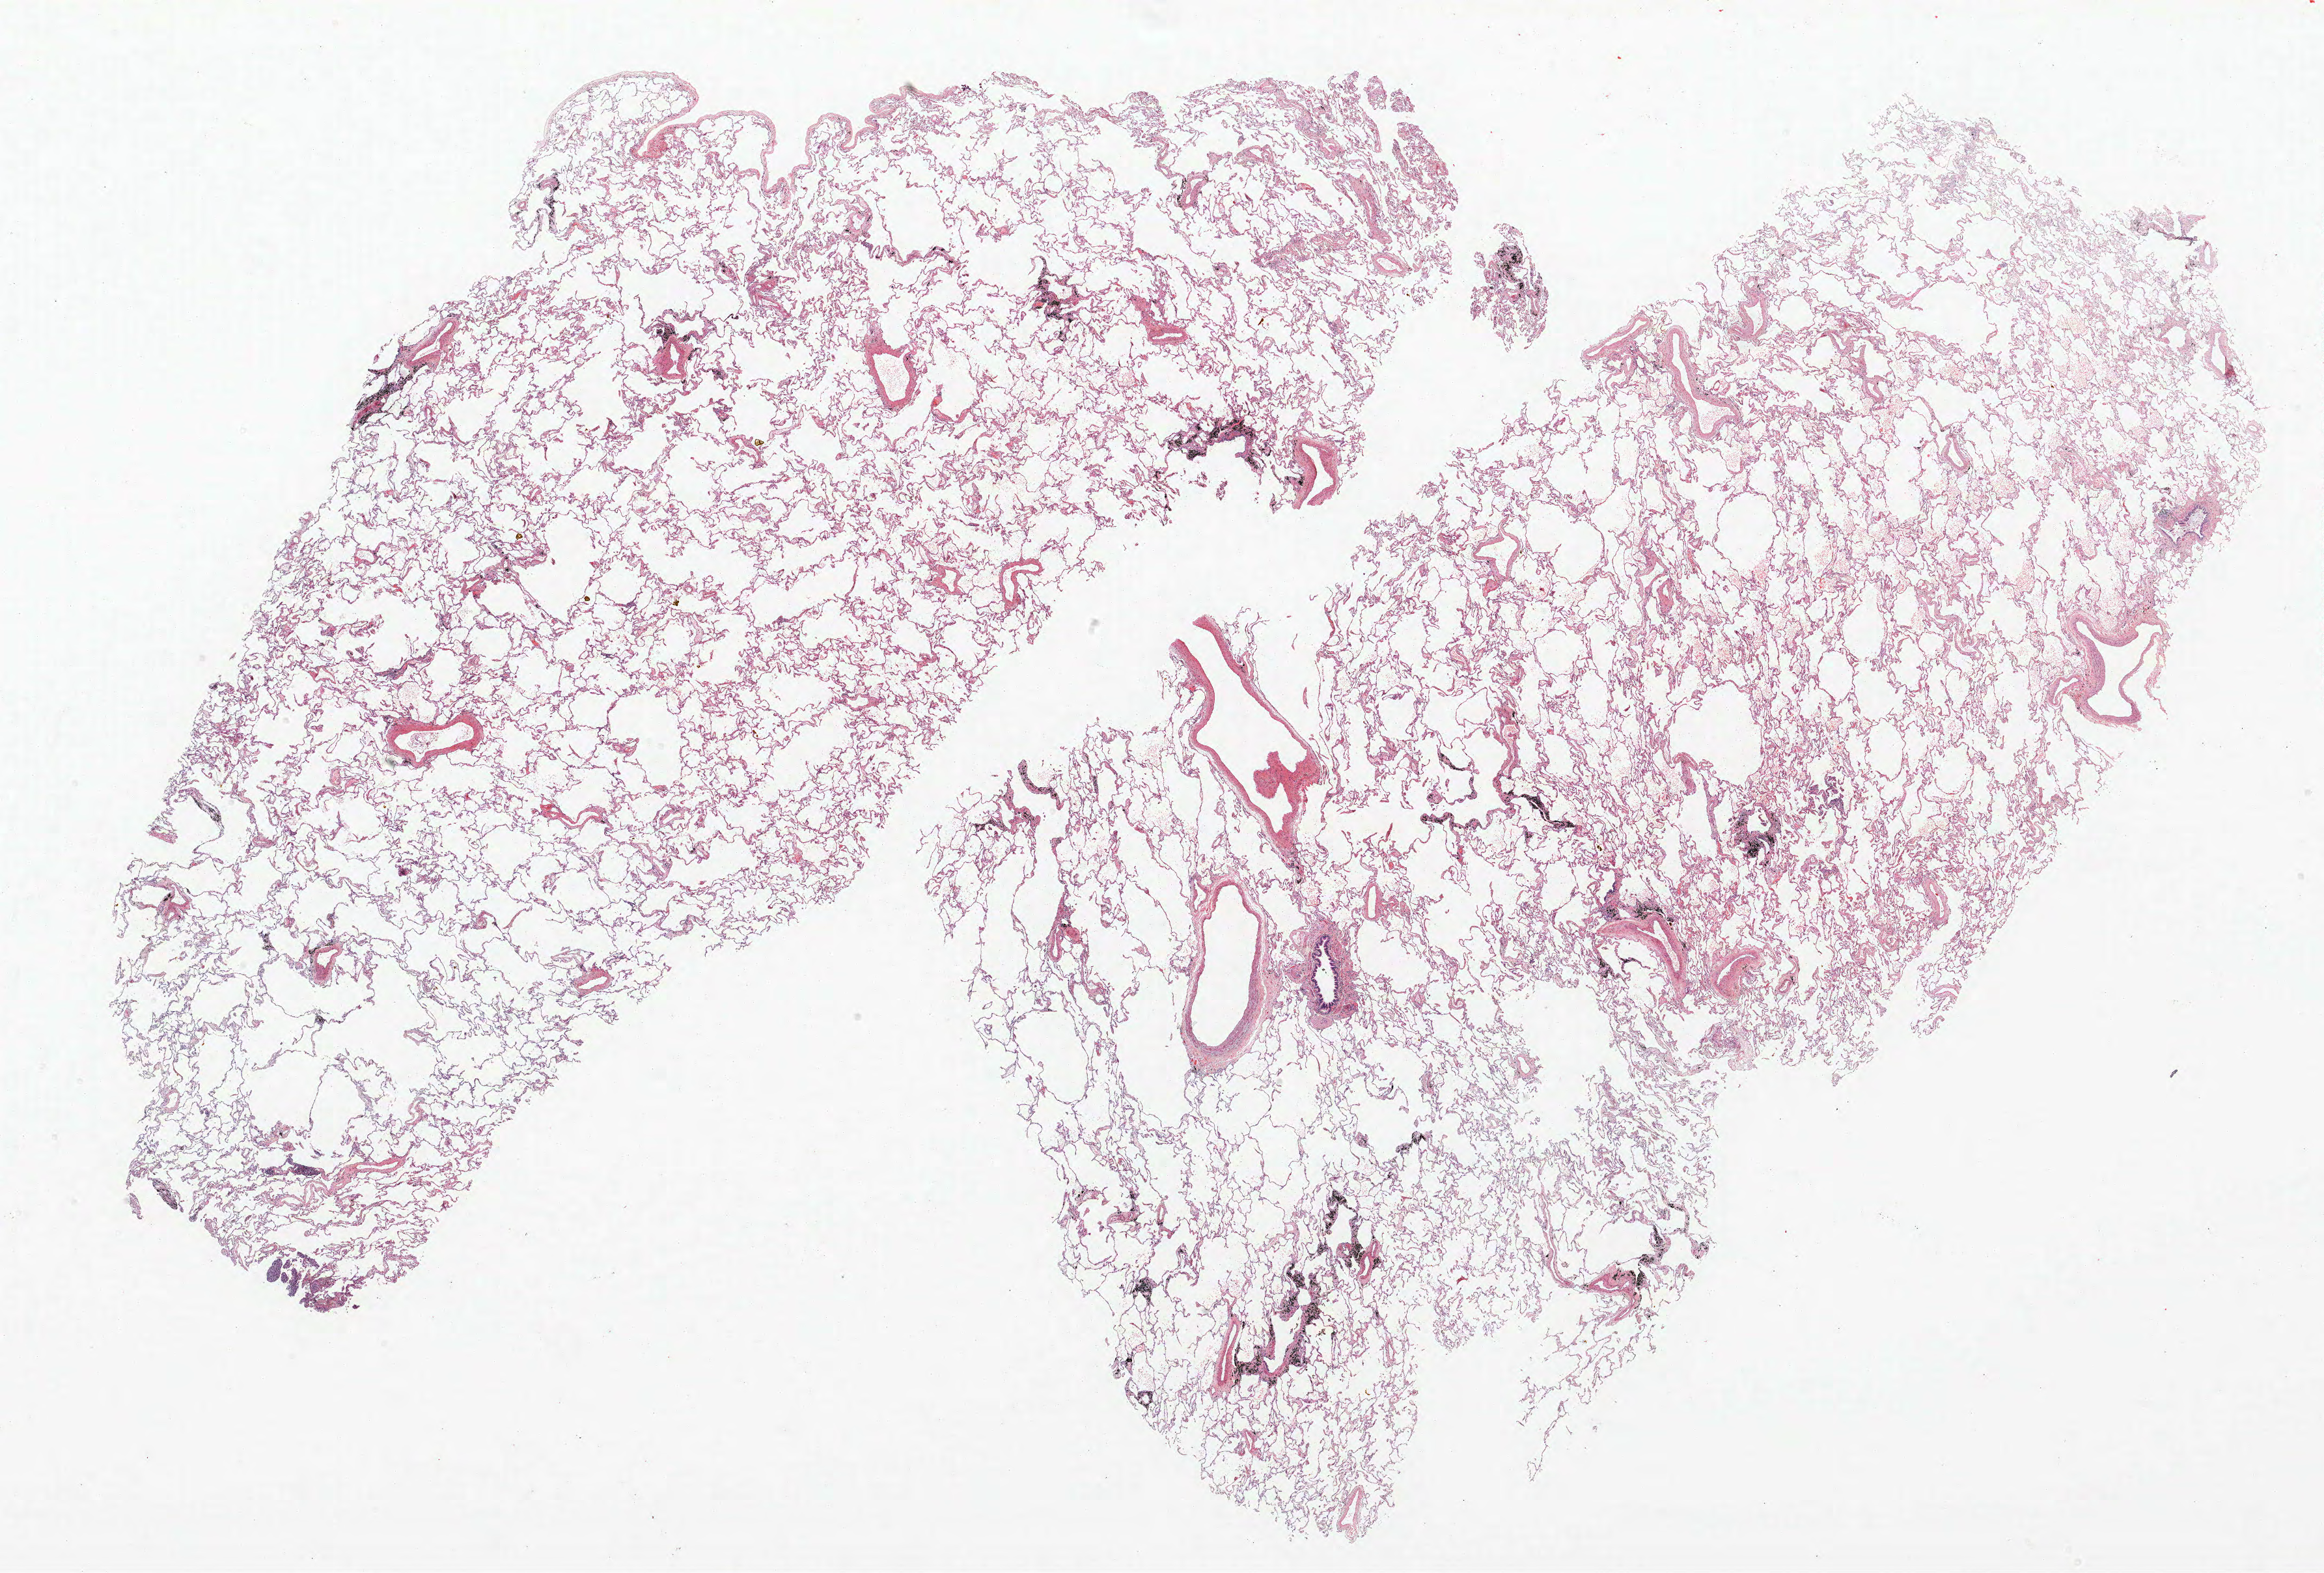
Whole-slide histology image, H&E — a low-resolution overview of the entire scanned area, about 28.6 x 19.3 mm, FFPE section, lung tissue. Female, age 70 at enrolment. Former smoker at enrolment. Grade: moderately differentiated (G2).
* stage (AJCC 6th edition): IA
* tumour size (pathology): 16 mm
* primary tumour location (clinical record): right lower lobe
* participant's lung-cancer diagnosis: Squamous cell carcinoma, NOS